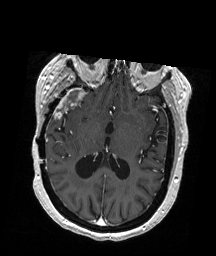
Brain MRI from a brain-tumour surgery series, one axial slice. Position 100 of 192 along the scan axis. T1-weighted post-contrast. 216 × 256 image matrix. From the clinical record (not read from this slice): histopathology: Glioblastoma; WHO grade: 4; IDH mutation: no; tumour location: Right Temporal.
Outlined on this slice (expert manual segmentation):
- tumour: bounding box (x1, y1, x2, y2) in pixels: (56, 88, 85, 115)